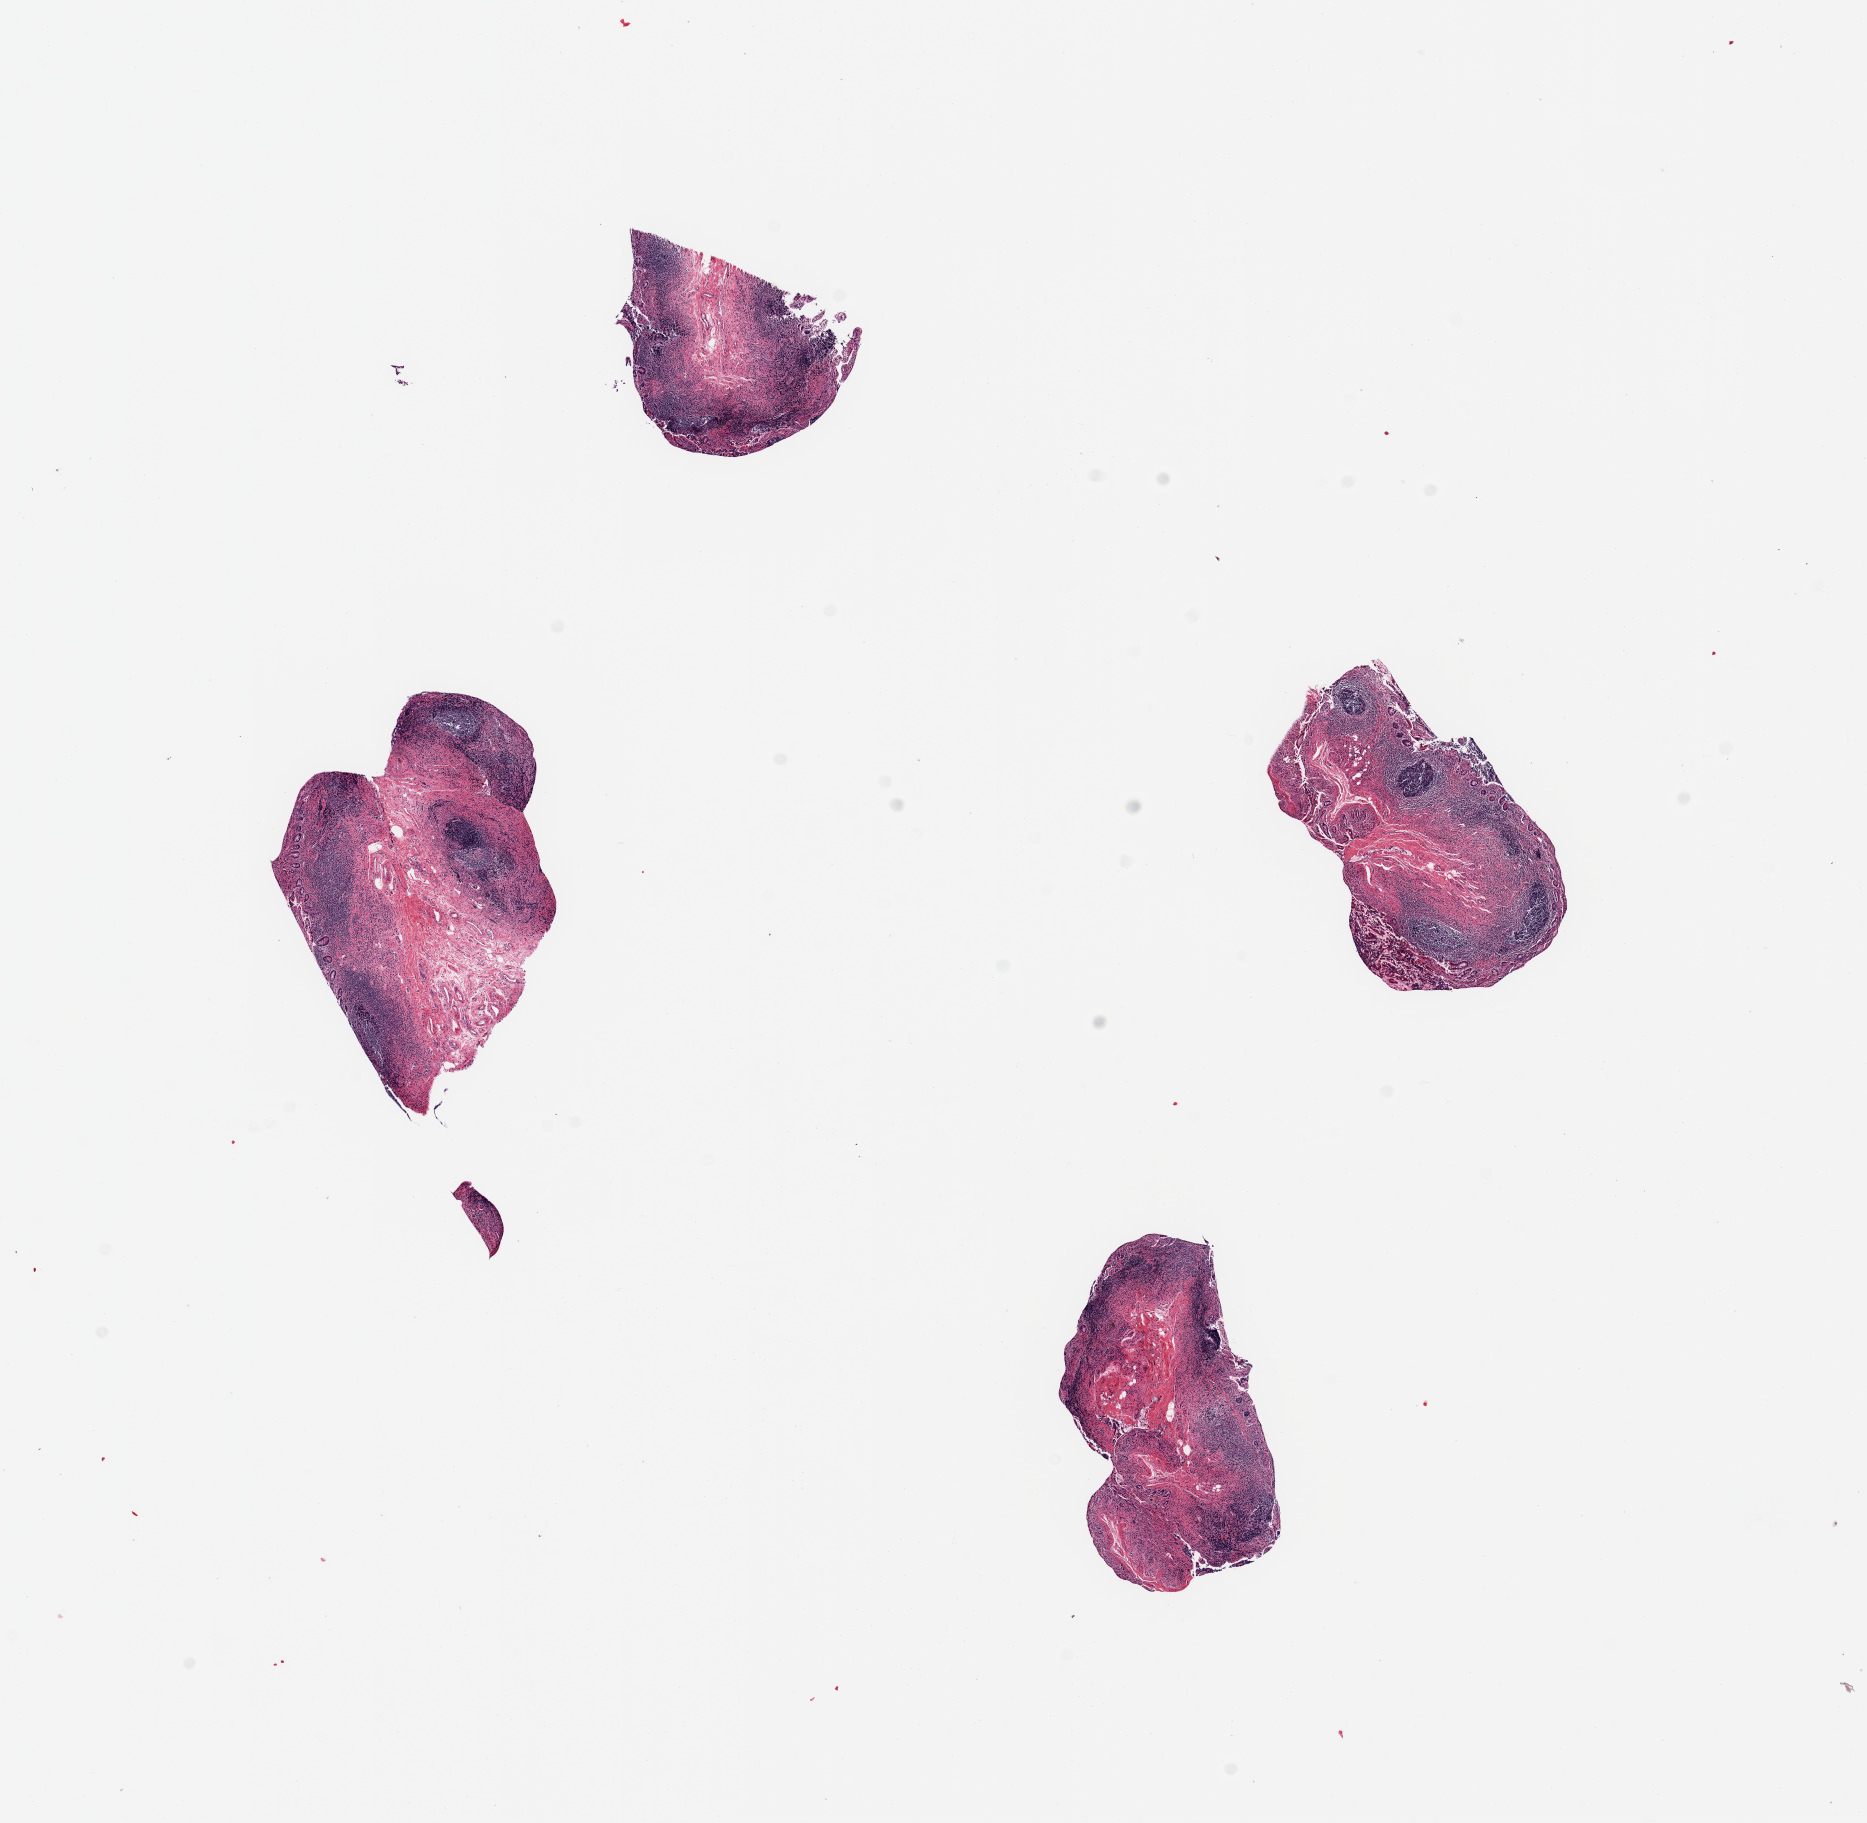
Haematoxylin and eosin whole-slide image, brightfield, a low-resolution overview of the entire scanned area, about 14.8 x 14.4 mm (acquisition: 20x scan); PAXgene-fixed, paraffin-embedded tissue; target tissue: ileum; donor tissue sample. Male donor.
Reviewer comment on this tissue sample: 4 pieces; 50% lymphoid content in mucosa & submucosa.